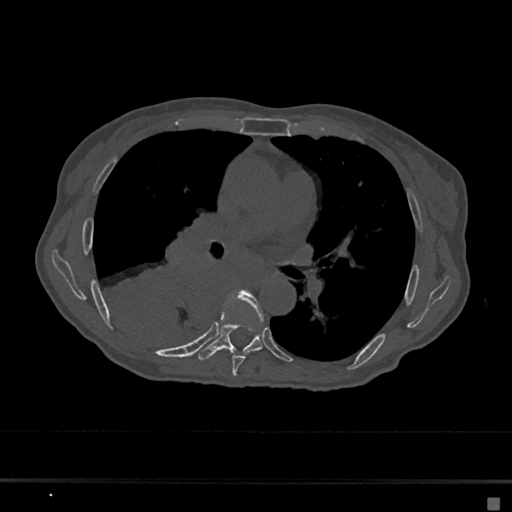
CT including the spine, one axial slice. Slice 394 of 797 in the series (ordered by position). 120 kVp. Bone window (W 1800 / L 400 HU). 0.5 mm slice thickness. 512 × 512 image matrix. Female patient, age 68 years. From the clinical record (not read from this slice): primary cancer: renal.
Structures marked on this image (semi-automatic segmentation, software-assisted and operator-edited):
- T6 vertebra: bounding box [x1, y1, x2, y2] px = [231, 290, 264, 376]
- T7 vertebra: [198, 314, 264, 361]